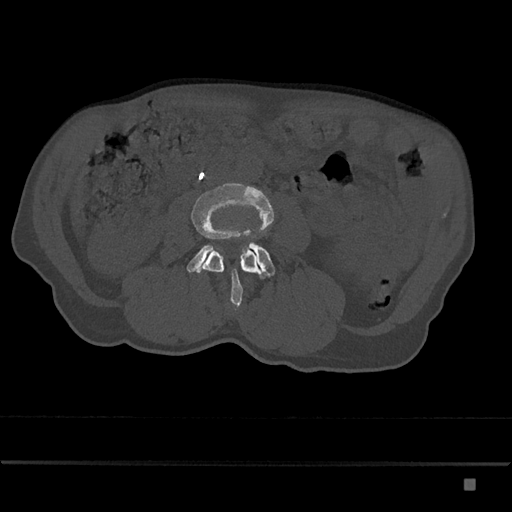
CT including the spine, one axial slice. Position 378 of 797 along the scan axis. Bone window (W 1800 / L 400 HU). 0.5 mm slice thickness. 512 × 512 image matrix. Patient: male, 72 years. Case-level facts recorded for this patient, not image findings: primary cancer: prostate.
Outlined on this slice (semi-automatic segmentation, software-assisted and operator-edited):
- L3 vertebra: bounding box [x1, y1, x2, y2] px = [191, 182, 274, 307]
- L4 vertebra: [187, 232, 275, 279]